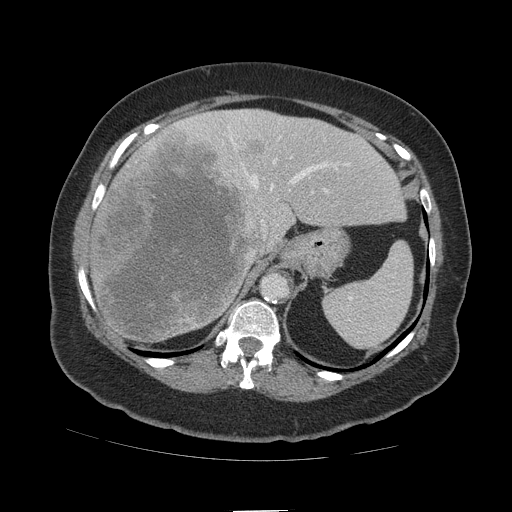
Contrast-enhanced abdominal CT (liver protocol), one axial slice; slice 78 of 109 in the series (ordered by position); reconstruction kernel STANDARD; 140 kVp; soft-tissue window (W 400 / L 40 HU); 512 × 512 image matrix. From the clinical record (not read from this slice): diagnosis: hepatocellular carcinoma (patient treated with transarterial chemoembolisation; whether this scan precedes or follows treatment is not stated here); TNM stage (as recorded): Stage-IVB; Child-Pugh class: A; tumour differentiation: poorly differentiated; tumour nodularity: multinodular.
Outlined on this slice (semi-automatic segmentation, software-assisted and operator-edited):
- liver parenchyma outside the tumour (the mass and vessels are separate outlines, so this box may not span the whole liver): bounding box <88,110,404,340> (left, top, right, bottom; pixels)
- mass: <91,130,272,345>
- liver vessels: <176,111,350,192>